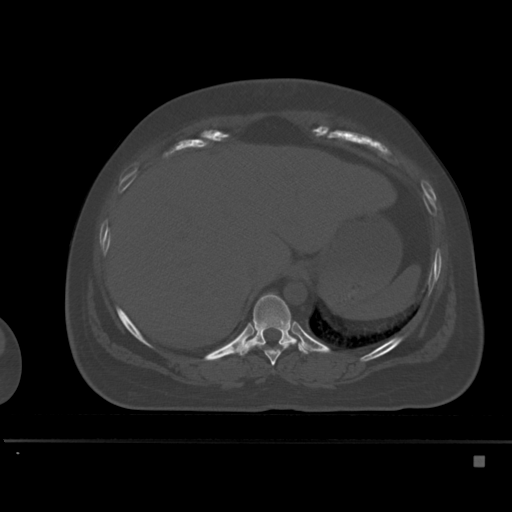
CT including the spine, one axial slice; slice 254 of 495 in the series (ordered by position); bone window (W 1800 / L 400 HU); 1.5 mm slice thickness; 512 × 512 image matrix. Patient: female, 33 years. Case-level facts recorded for this patient, not image findings: primary cancer: breast; vertebrae with lytic lesions (as recorded): T1.
Annotated regions visible in this slice (semi-automatic segmentation, software-assisted and operator-edited):
- T10 vertebra: box from (x=237, y=293) to (x=309, y=356) px
- T9 vertebra: (x=253, y=342)–(x=296, y=366)